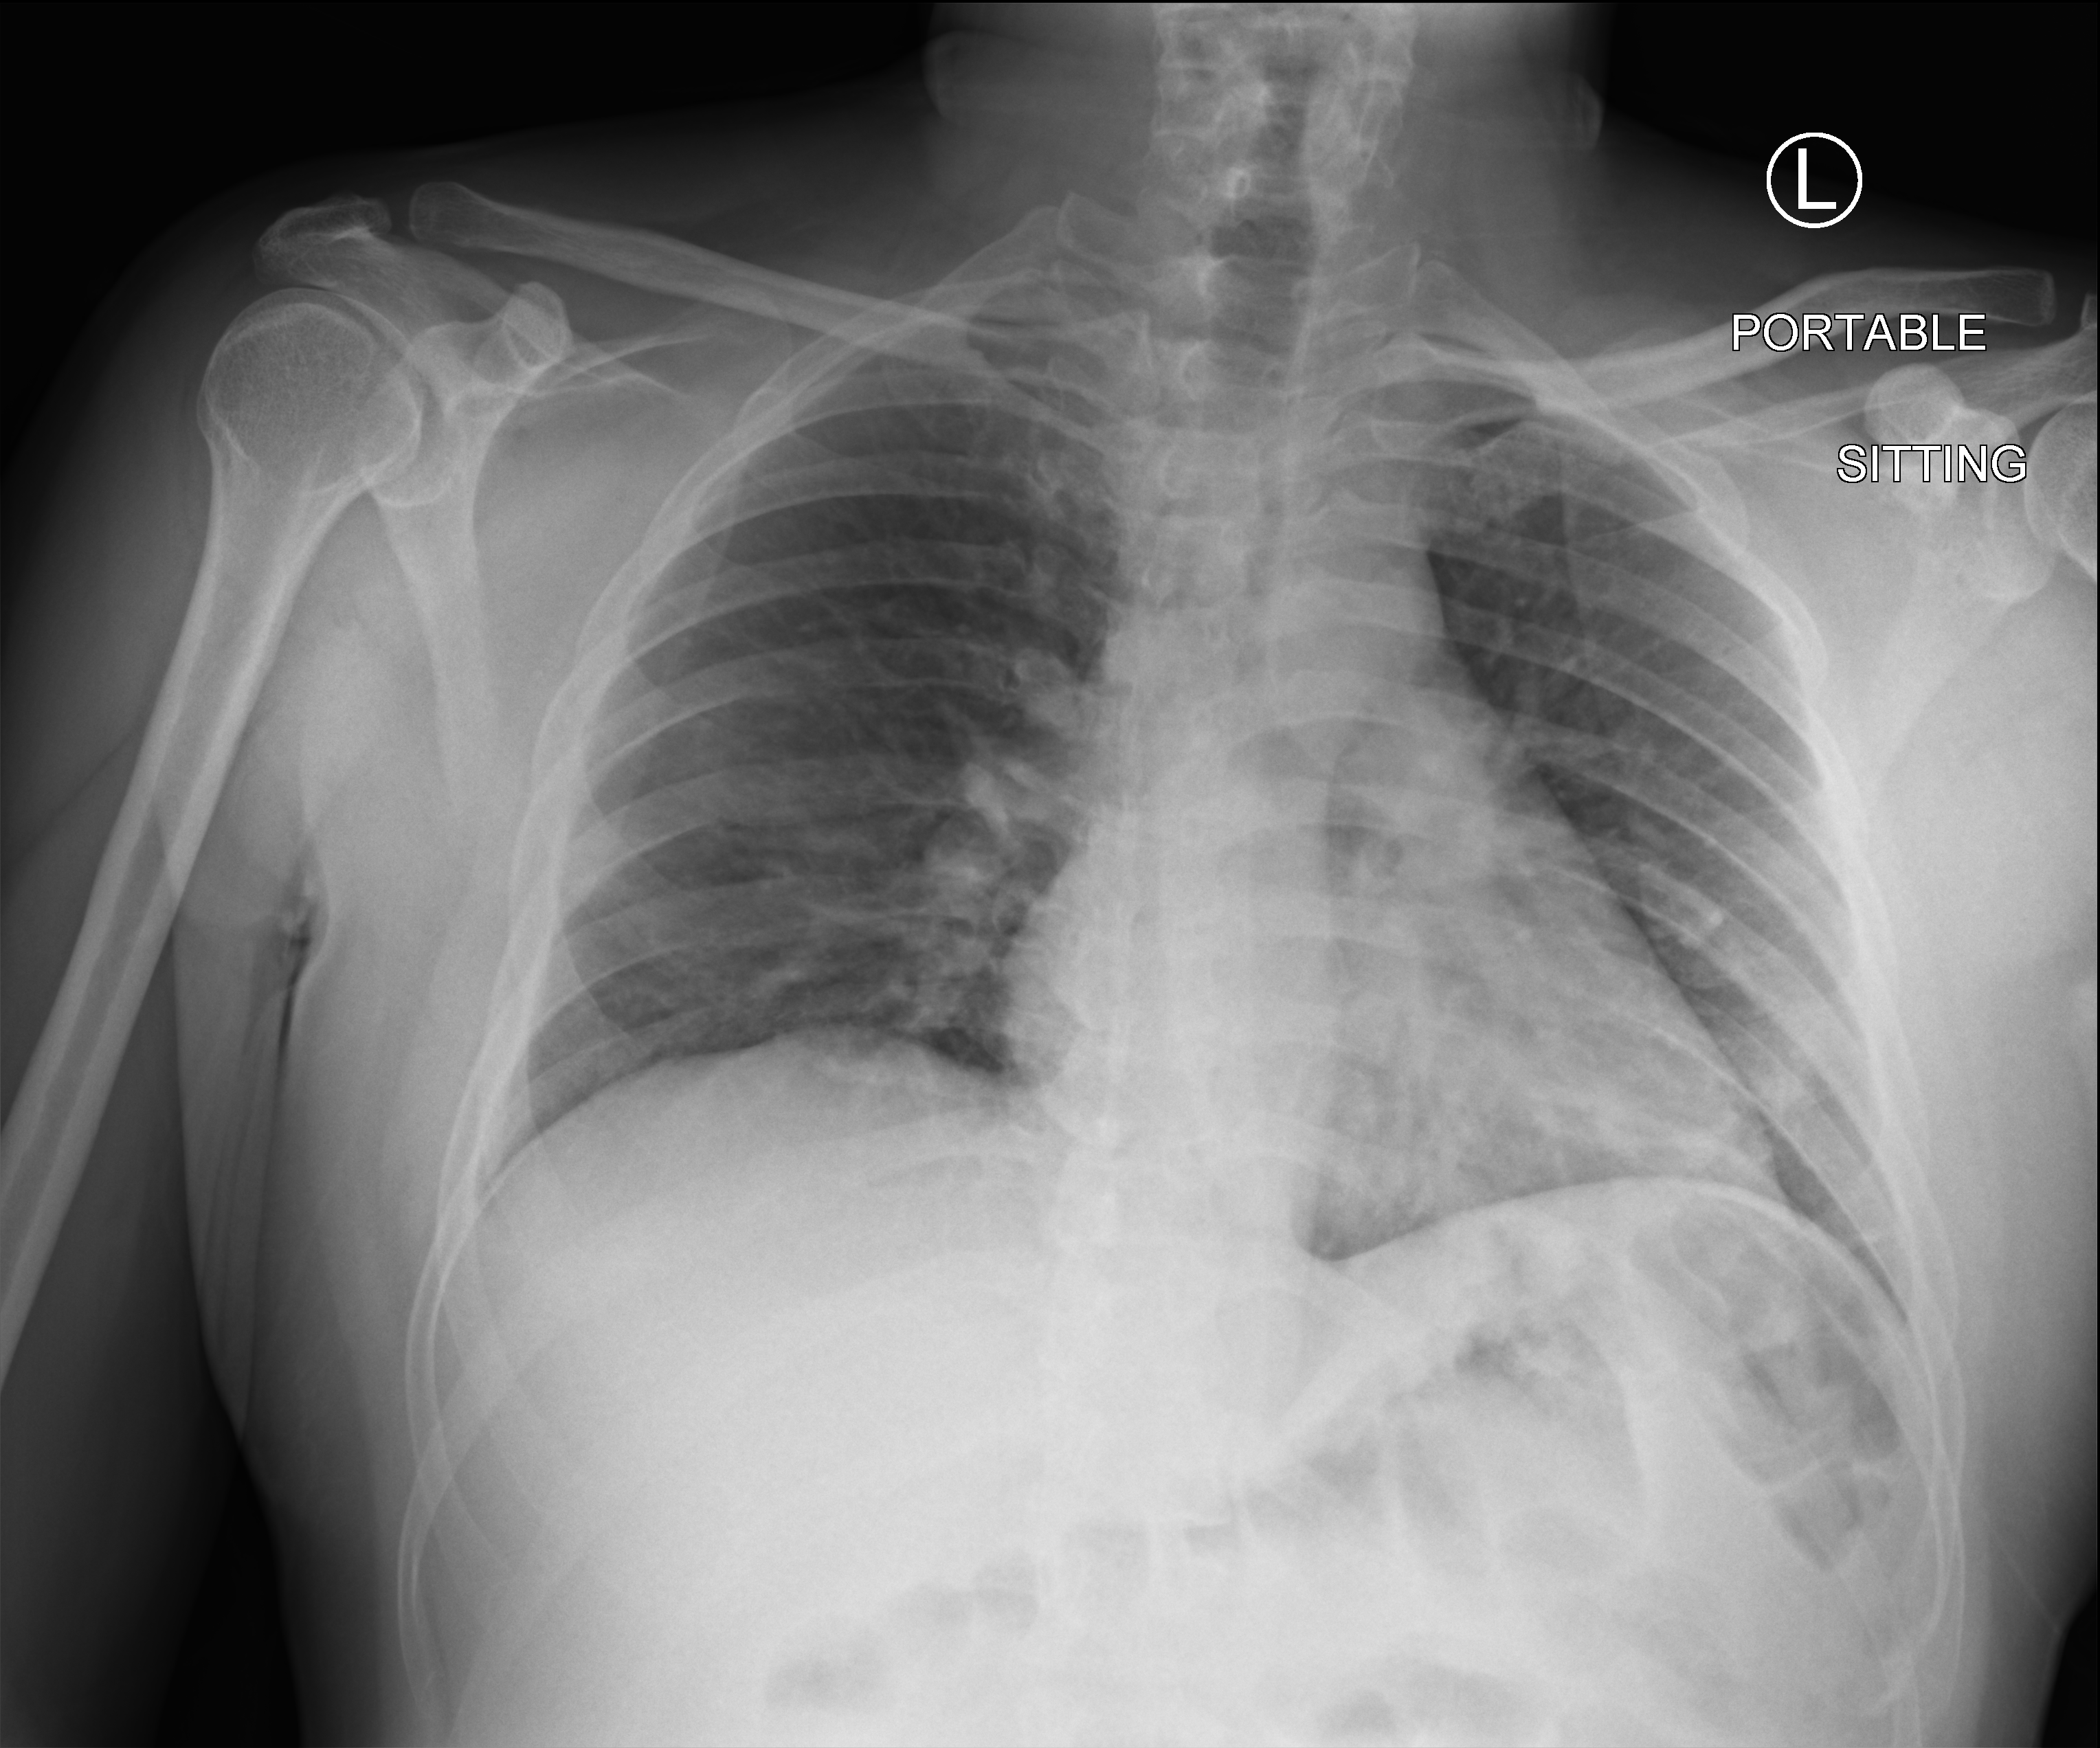
Chest X-ray (portable), anteroposterior (AP) projection. Patient hospitalised with COVID-19; male, aged 18–59 years.
Admission-level facts for this patient (not findings on this image; timing relative to this image not recorded):
- mechanically ventilated during this hospital stay: no